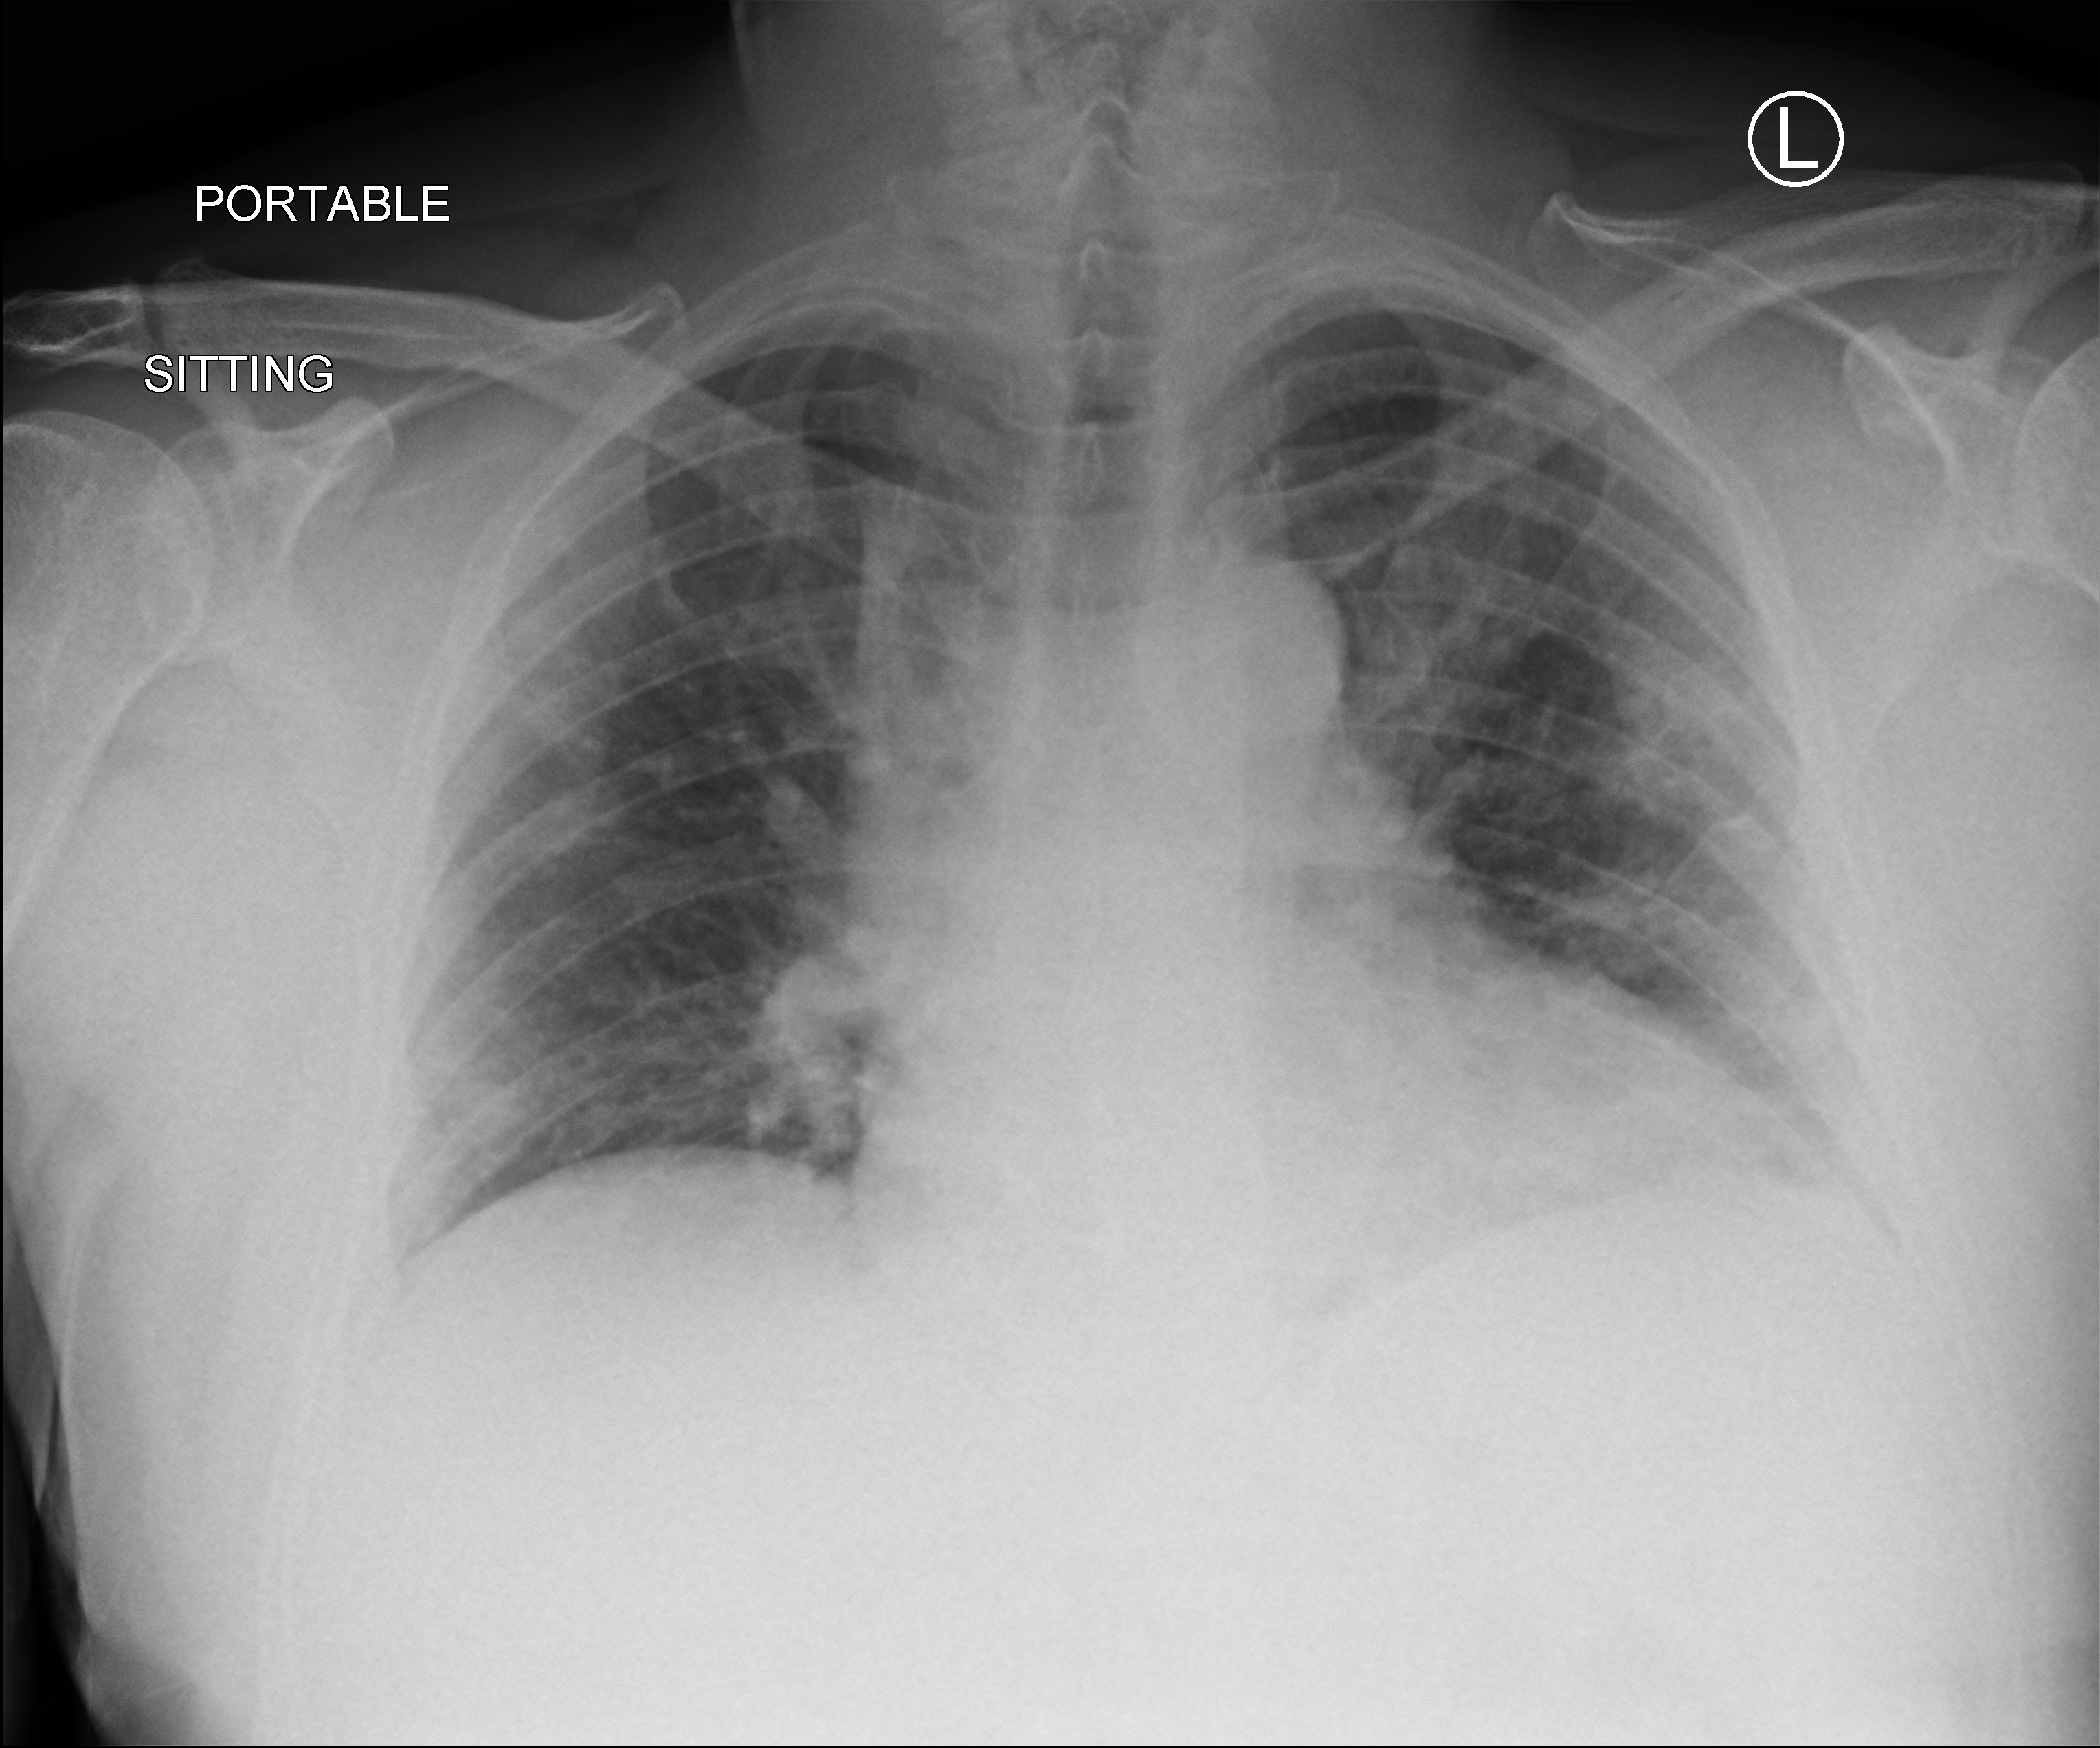
Chest X-ray (portable); anteroposterior (AP) projection. Patient hospitalised with COVID-19; male, aged 60–74 years.
Admission-level facts for this patient (not findings on this image; timing relative to this image not recorded): mechanically ventilated during this hospital stay: no; admitted to intensive care during this hospital stay: no.